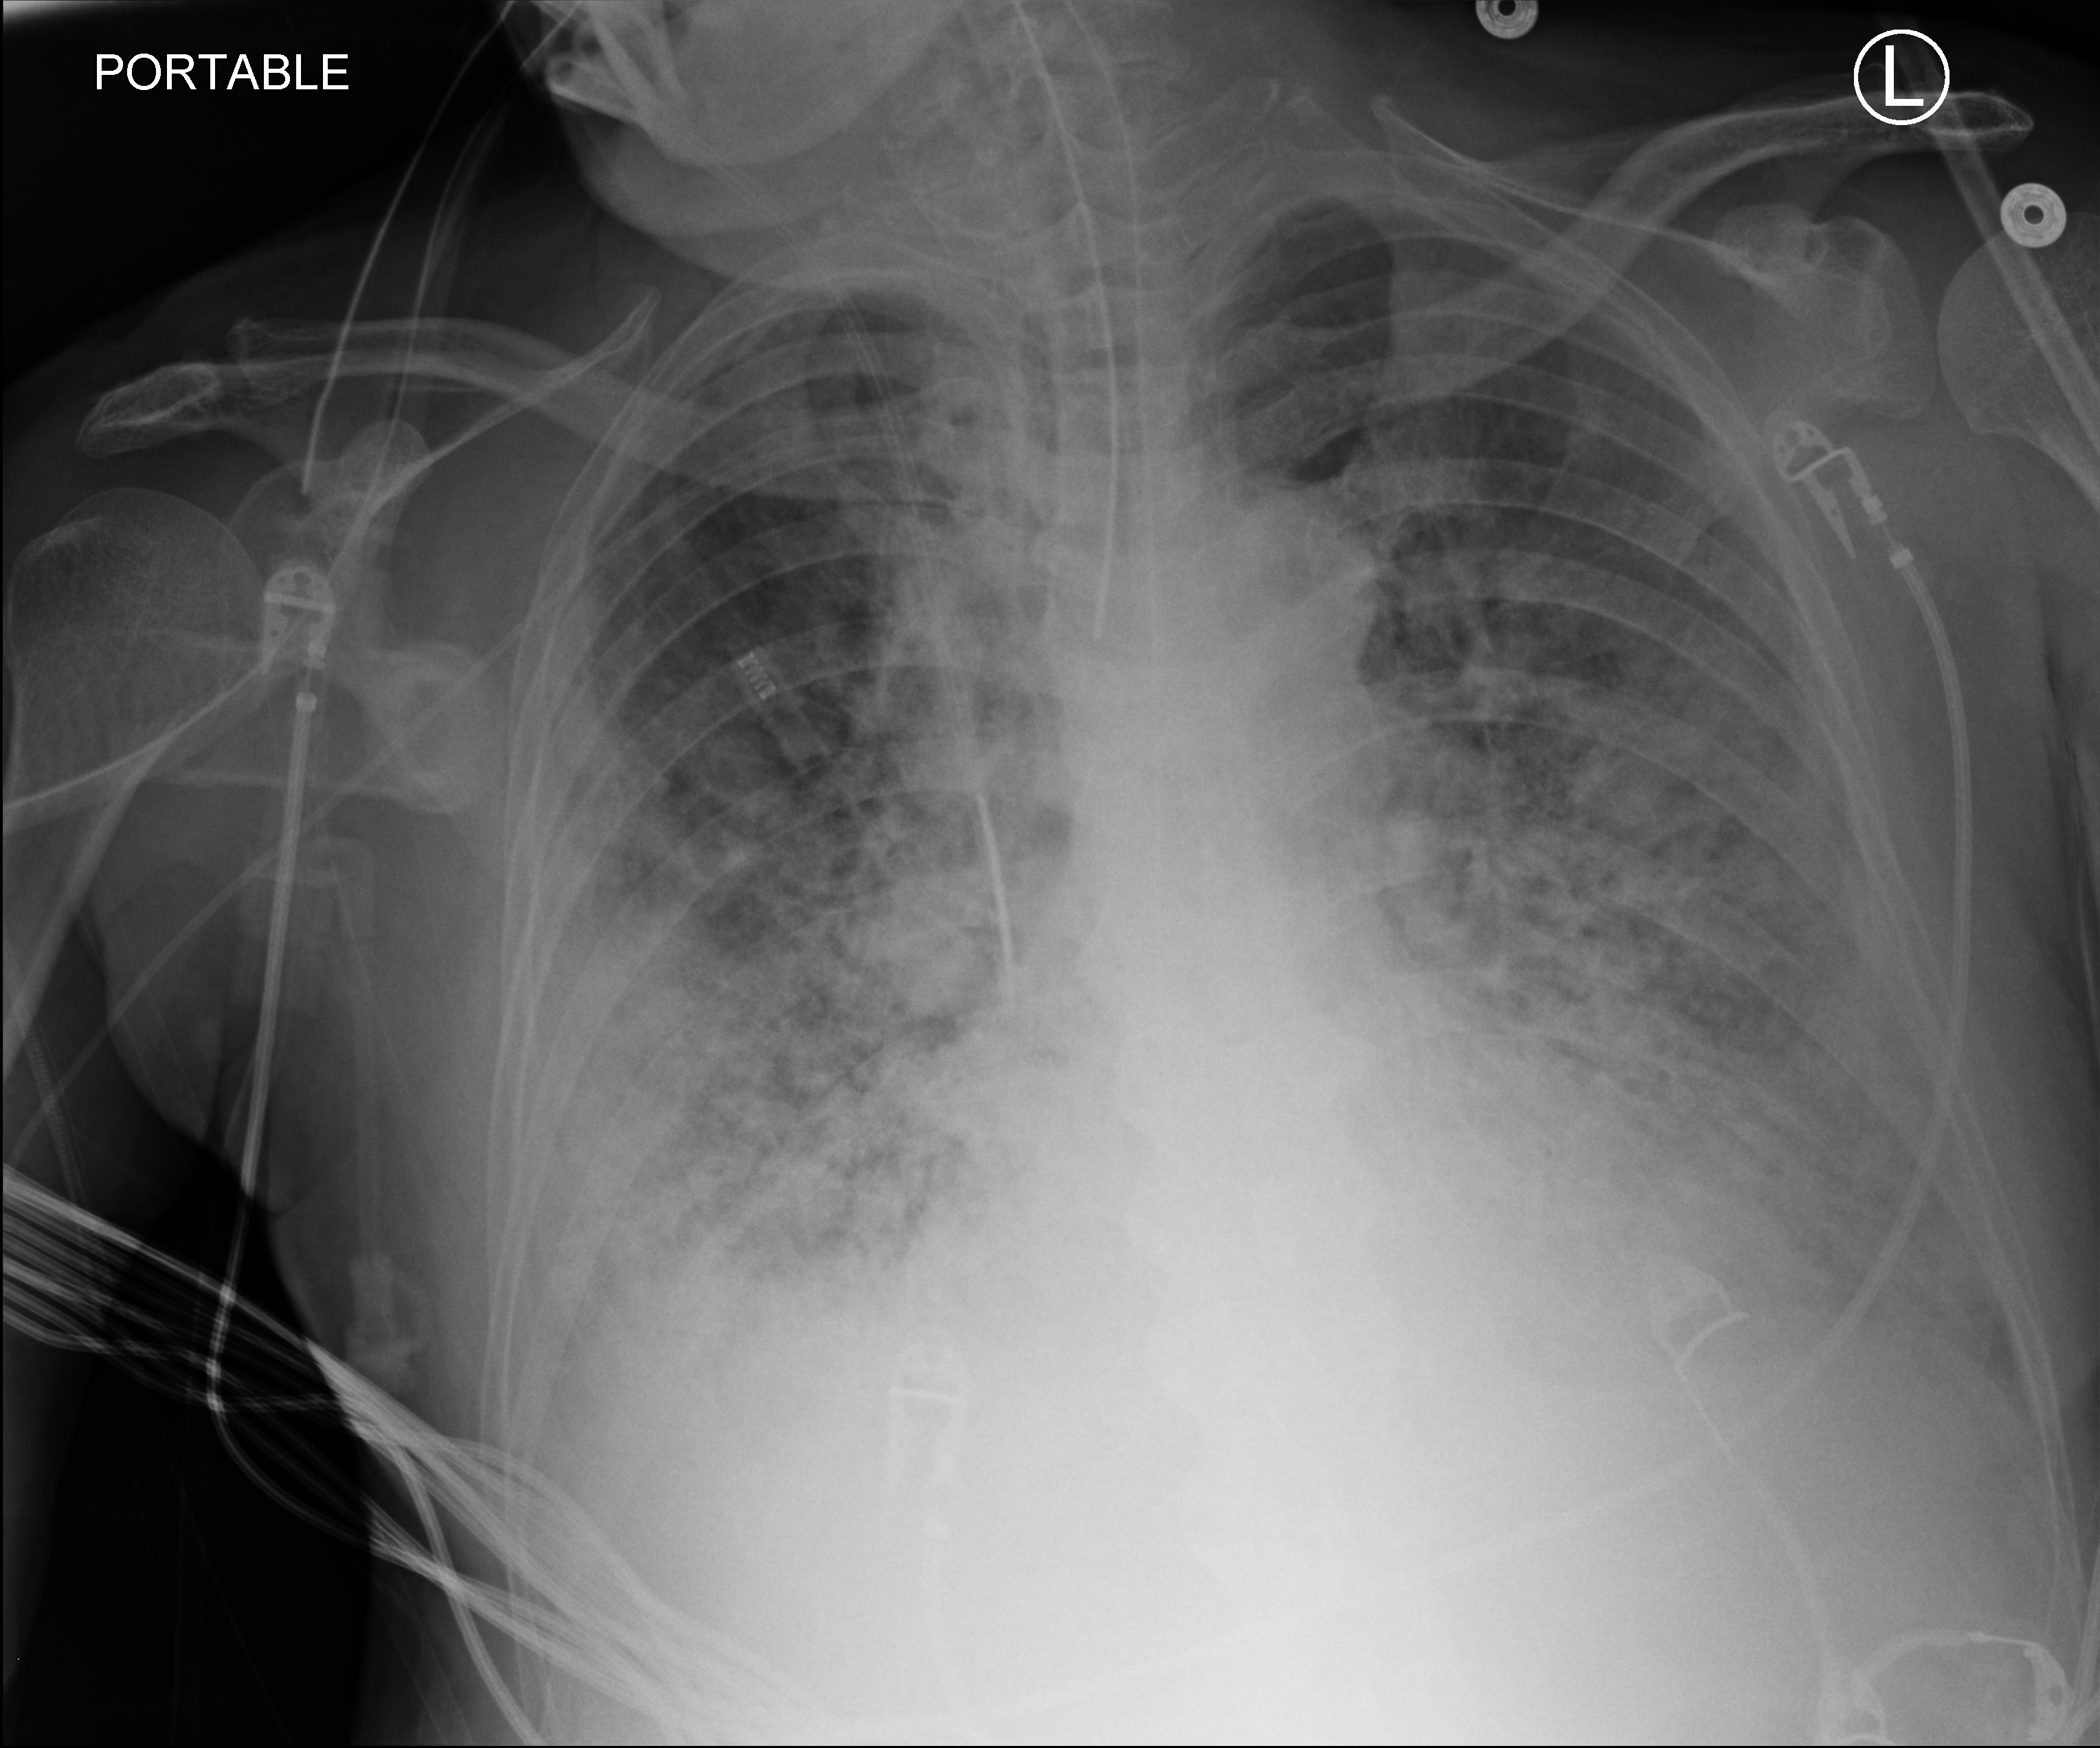
Bedside chest radiograph (computed radiography), anteroposterior (AP) projection. Male patient hospitalised with COVID-19, age 60–74 years.
Admission-level facts for this patient (not findings on this image; timing relative to this image not recorded): admitted to intensive care during this hospital stay: yes; hypertension (admission record): yes.